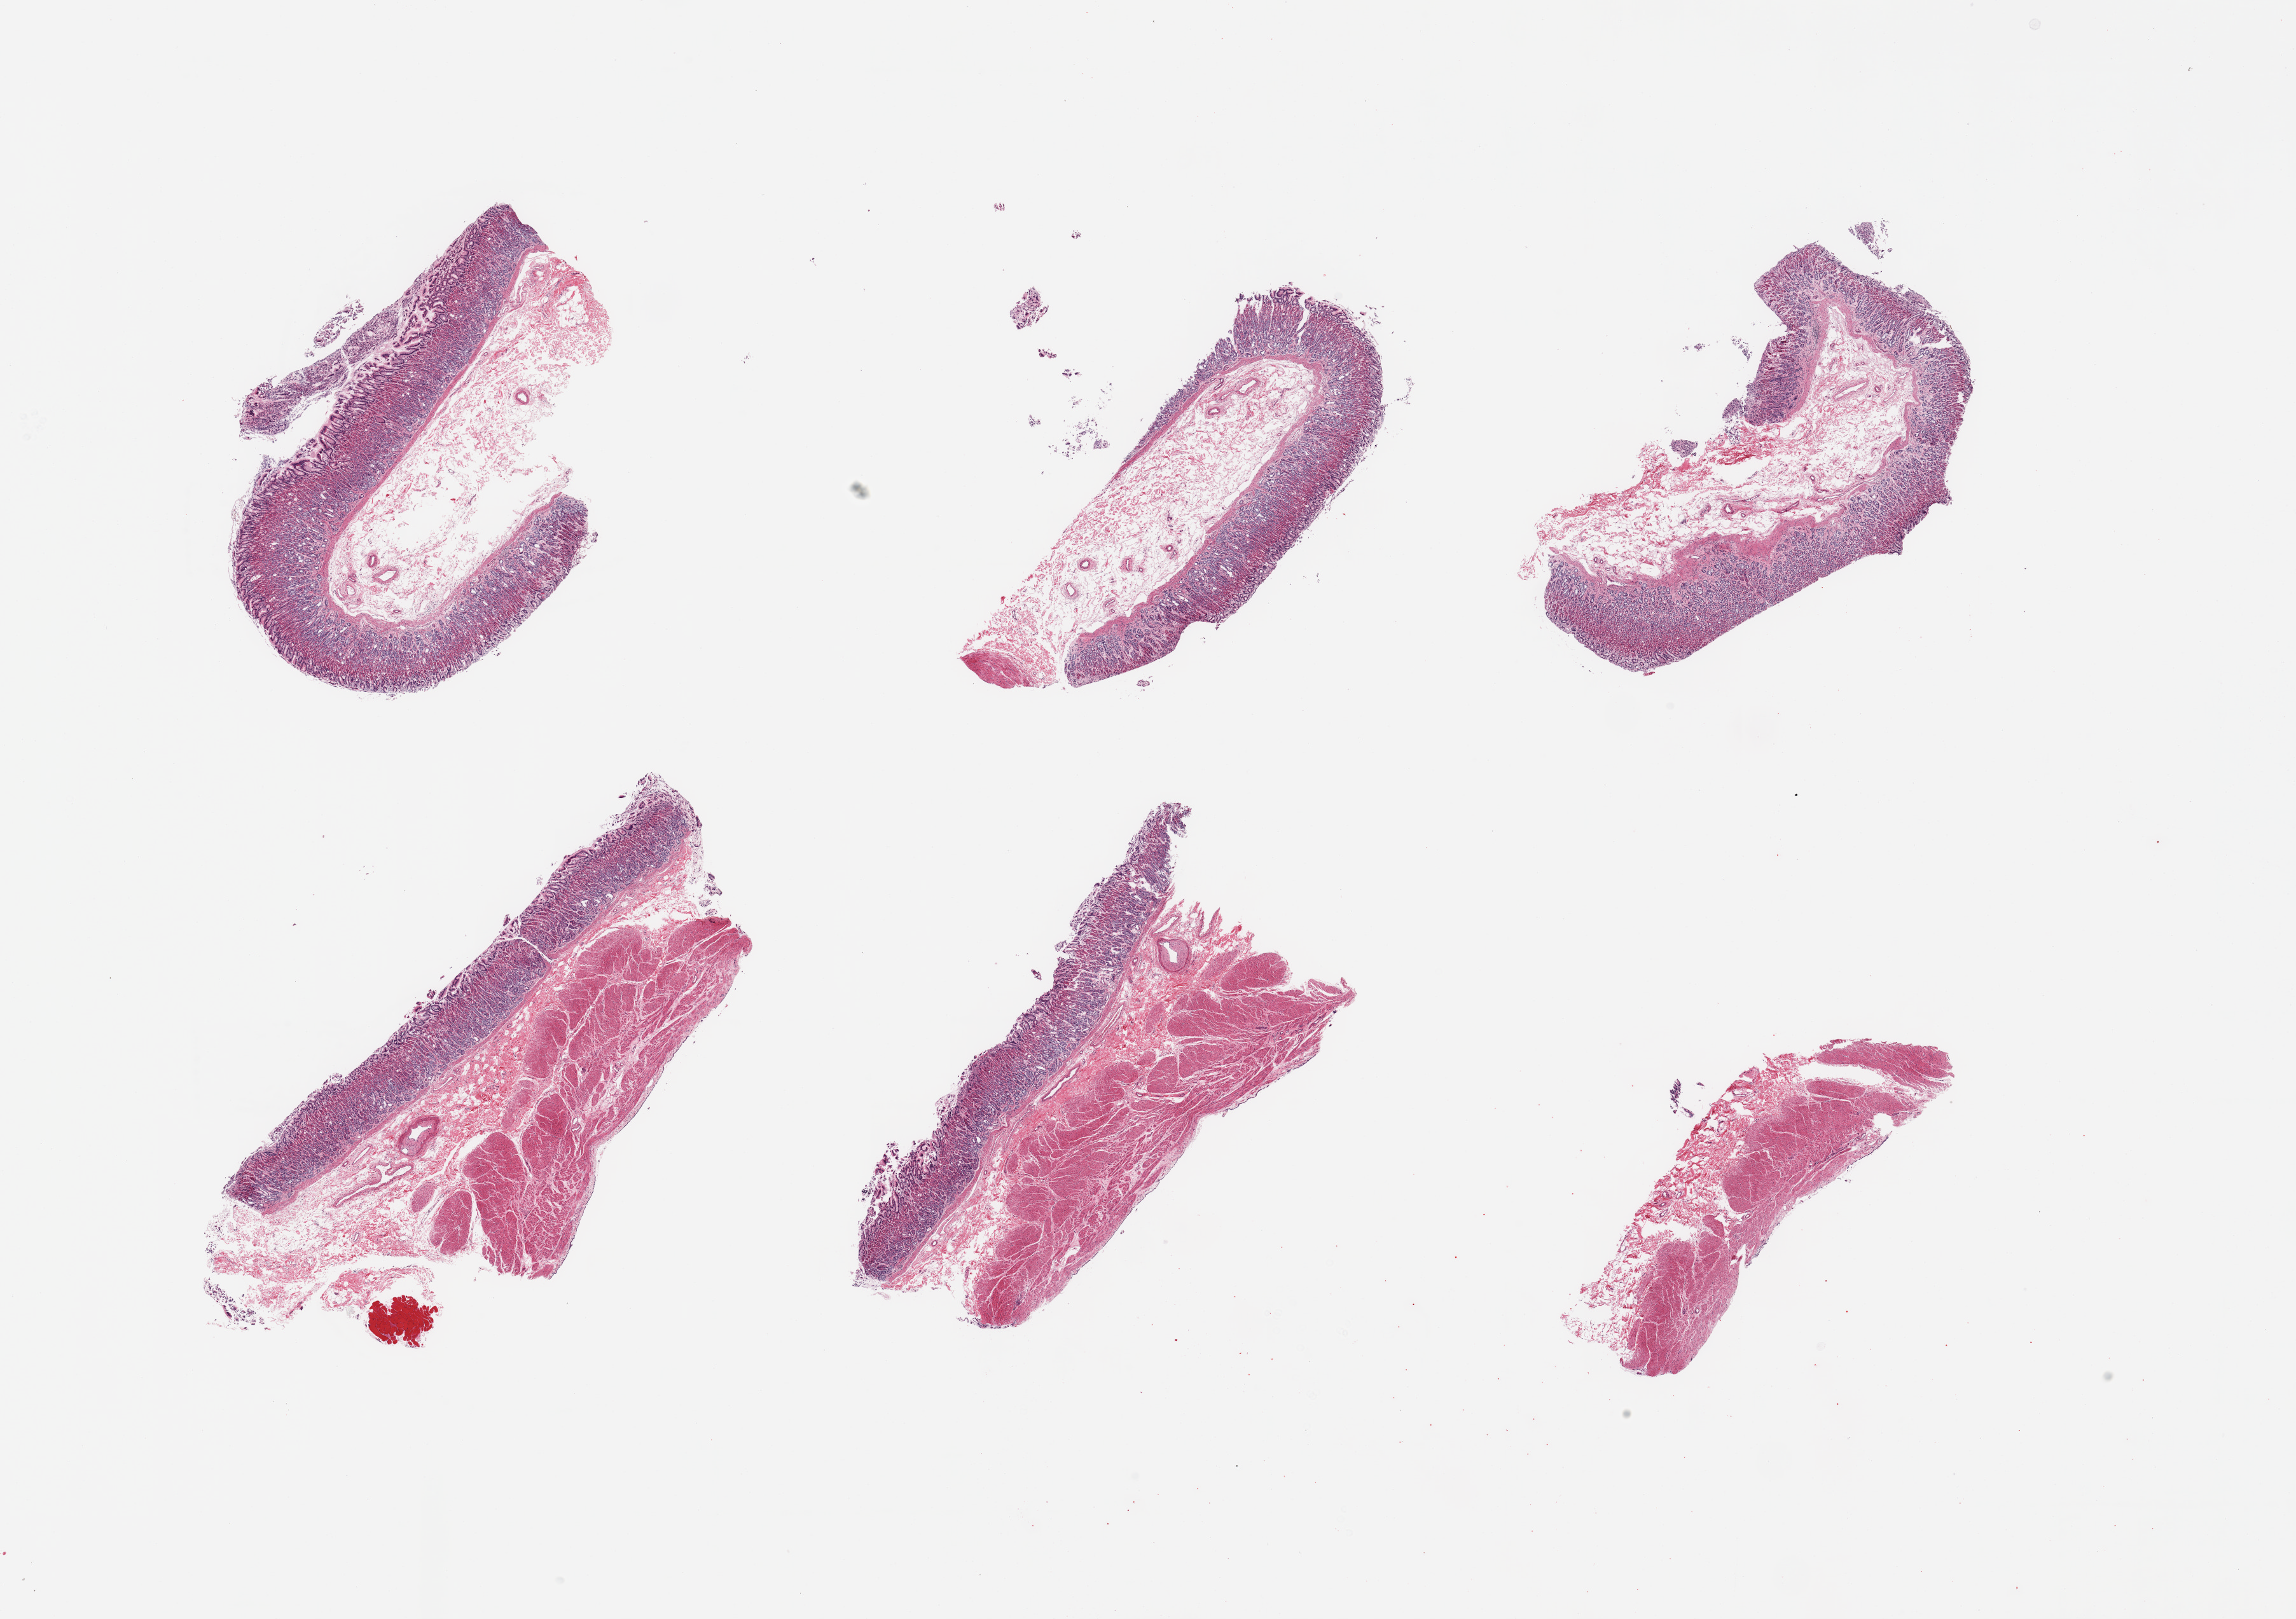
Whole-slide image, H&E stain, low-resolution overview of the scanned area, about 28.5 x 20.1 mm, PAXgene-fixed paraffin-embedded (PFPE) section, section of stomach (target tissue), tissue donor sample. Male donor.
Pathologist's review note for this sample: 6 pieces; 3 have mucosa/submucosa only; 1 has muscularis only; 2 have full thickness (mucosa & muscularis).